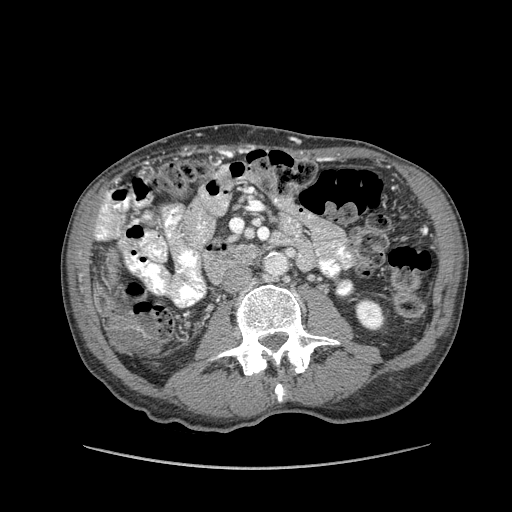
Contrast-enhanced abdominal CT (liver protocol), one axial slice; position 7 of 162 along the scan axis; reconstruction kernel STANDARD; 100 kVp; soft-tissue window (W 400 / L 40 HU); 512 × 512 image matrix, field of view 400 × 400 mm. Case-level facts recorded for this patient, not image findings: diagnosis: hepatocellular carcinoma (patient treated with transarterial chemoembolisation; whether this scan precedes or follows treatment is not stated here); TNM stage (as recorded): Stage-IIIA; Child-Pugh class: A; tumour nodularity: multinodular; tumour size: 9.9 cm.
Outlined on this slice (semi-automatically segmented with operator editing):
- liver parenchyma outside the tumour (the mass and vessels are separate outlines, so this box may not span the whole liver): bounding box <96,192,136,352> (left, top, right, bottom; pixels)
- liver vessels: <96,193,116,239>